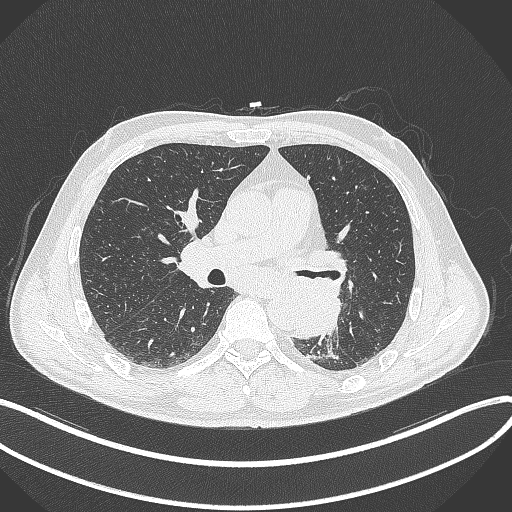
Chest CT, one axial slice. Reconstruction kernel B70f. 120 kVp. Lung window (W 1500 / L -600 HU). 1 mm slice thickness. 512 × 512 image matrix, field of view 400 × 400 mm. Male patient, age 59 years. From the clinical record (not read from this slice): clinical TNM (as recorded): T2a N2 M0.
Outlined on this slice (bounding box drawn by a radiologist):
- lung tumour (recorded histology: squamous cell carcinoma): bounding box [x1, y1, x2, y2] px = [289, 276, 342, 339]